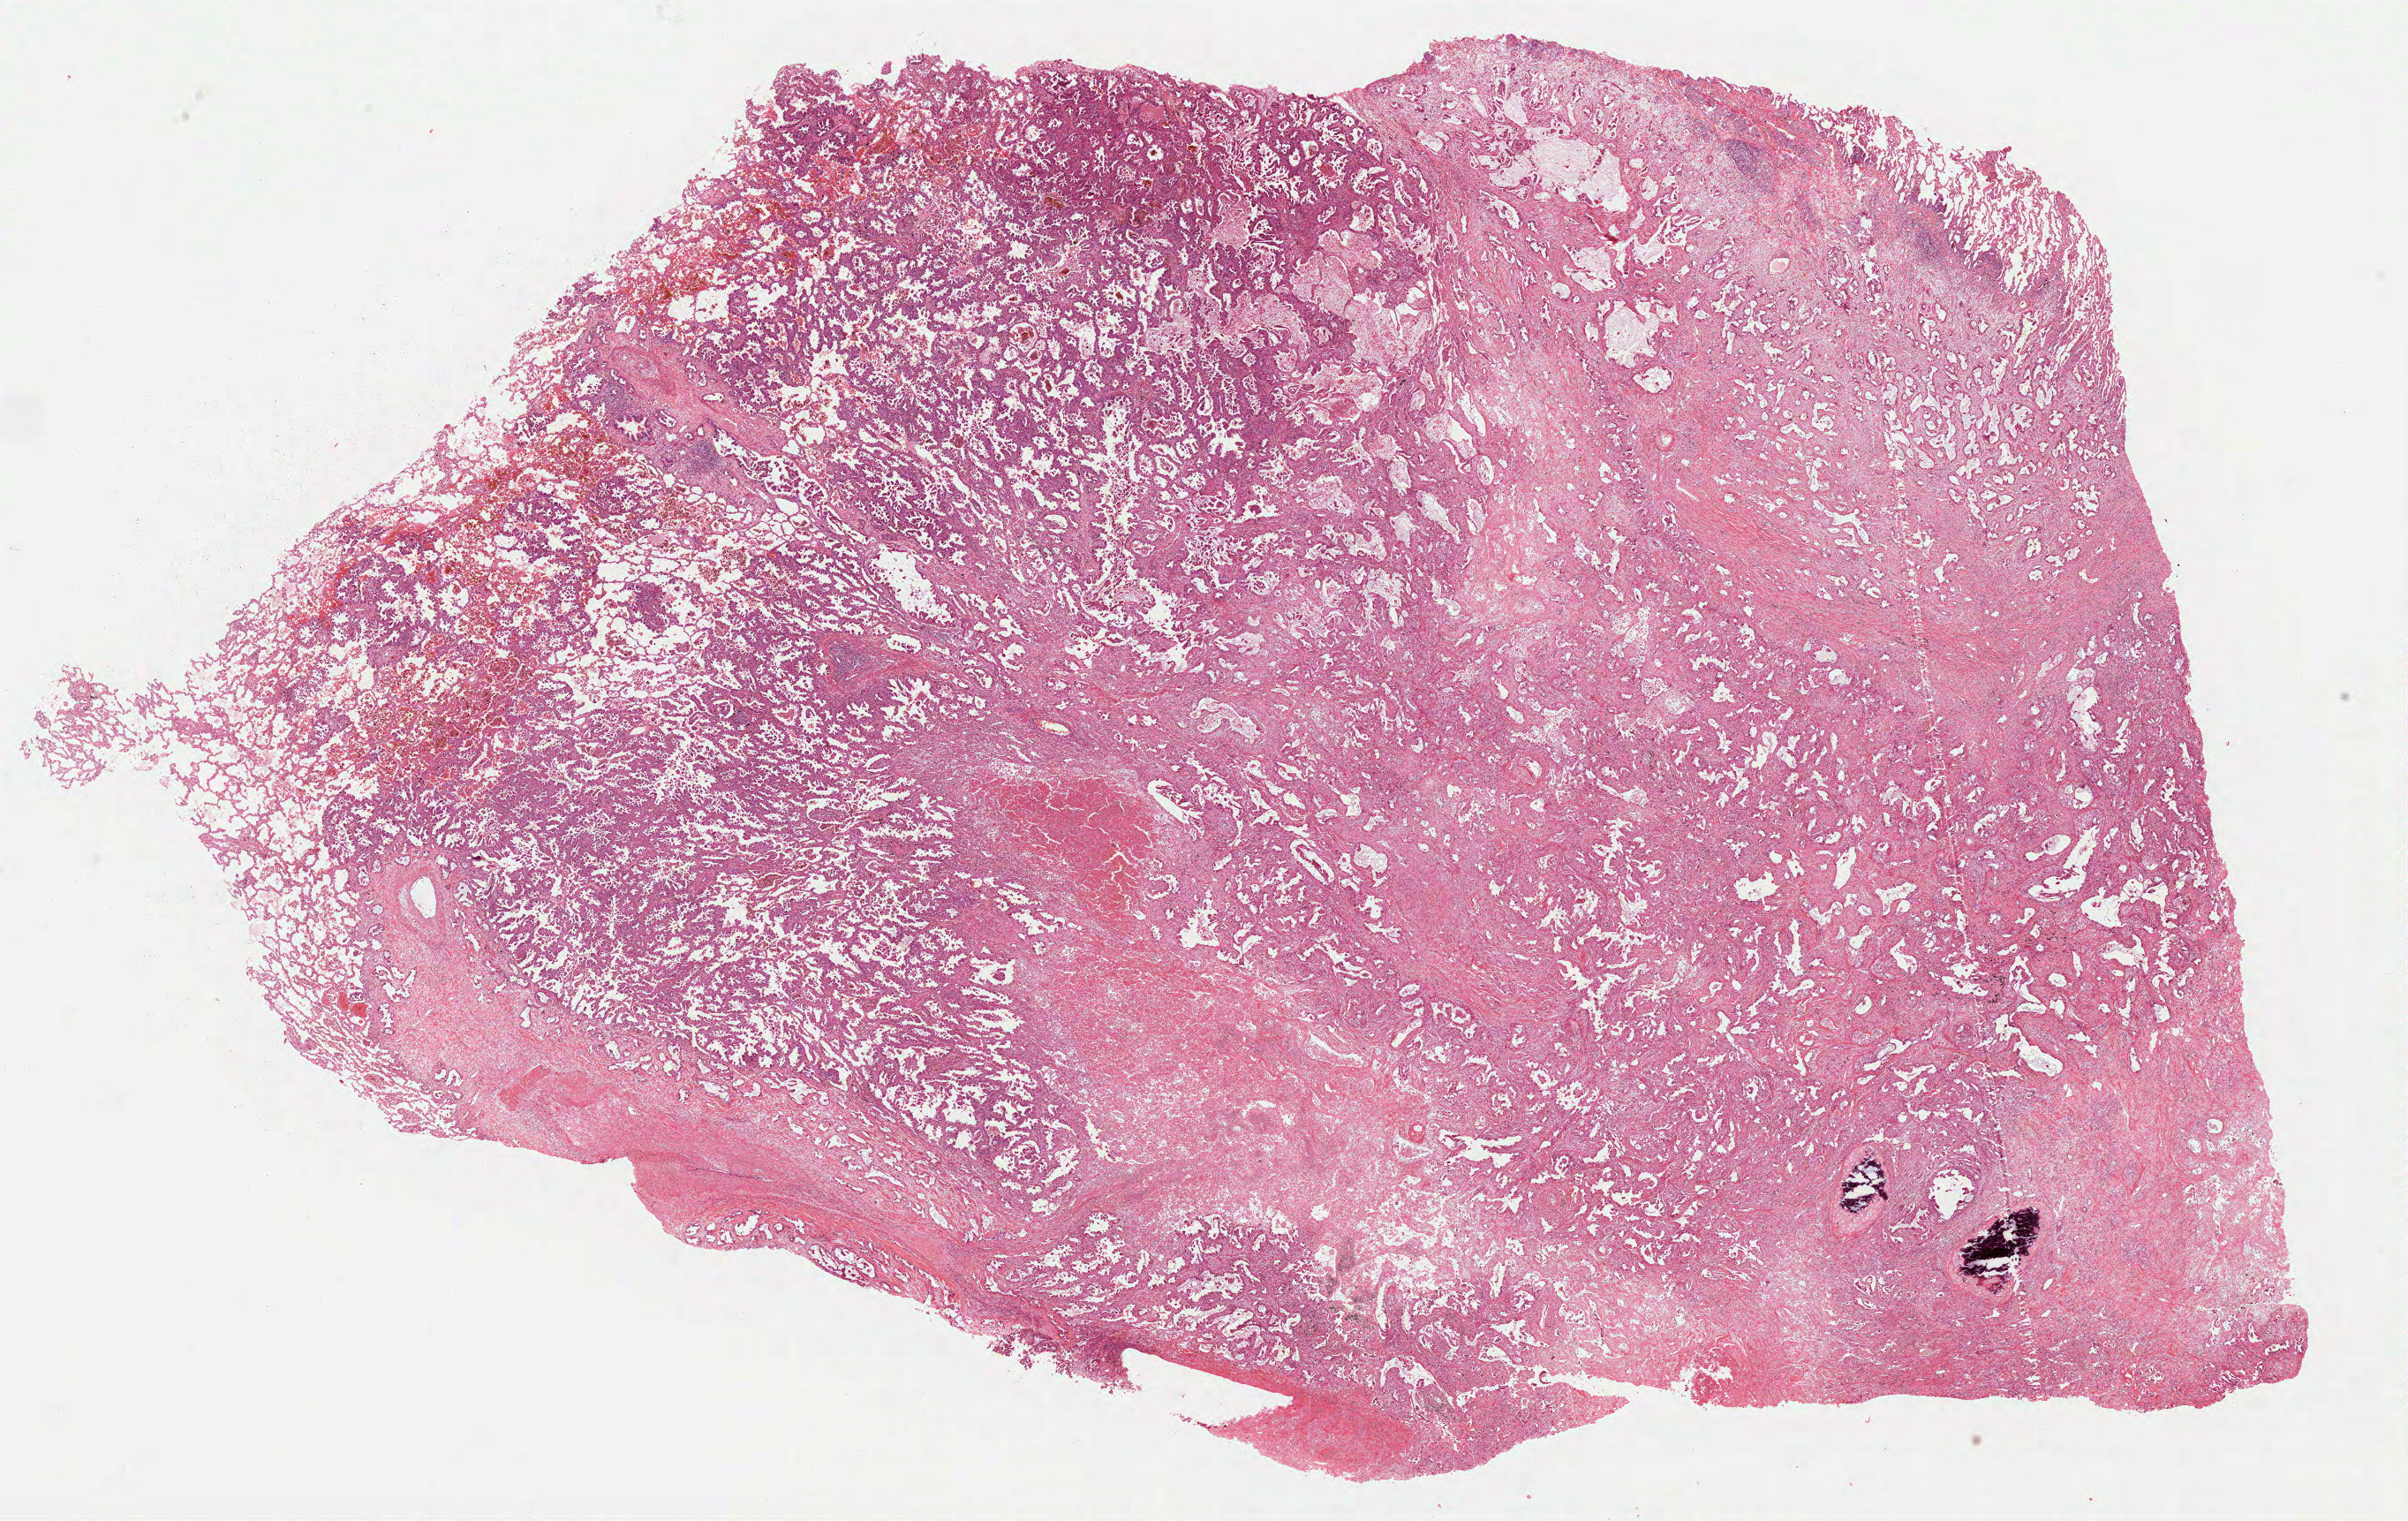
Hematoxylin and eosin (H&E) stained whole-slide image, whole scanned area (about 22.0 x 13.9 mm, acquisition: 40x scan) shown as a low-resolution overview, FFPE section, sample: primary tumour, lung. Male patient; age at initial diagnosis 52 years.
* AJCC pathologic stage: IIA
* TNM: T2a N1 M0
* diagnosis: Adenocarcinoma, NOS (upper lobe, lung)